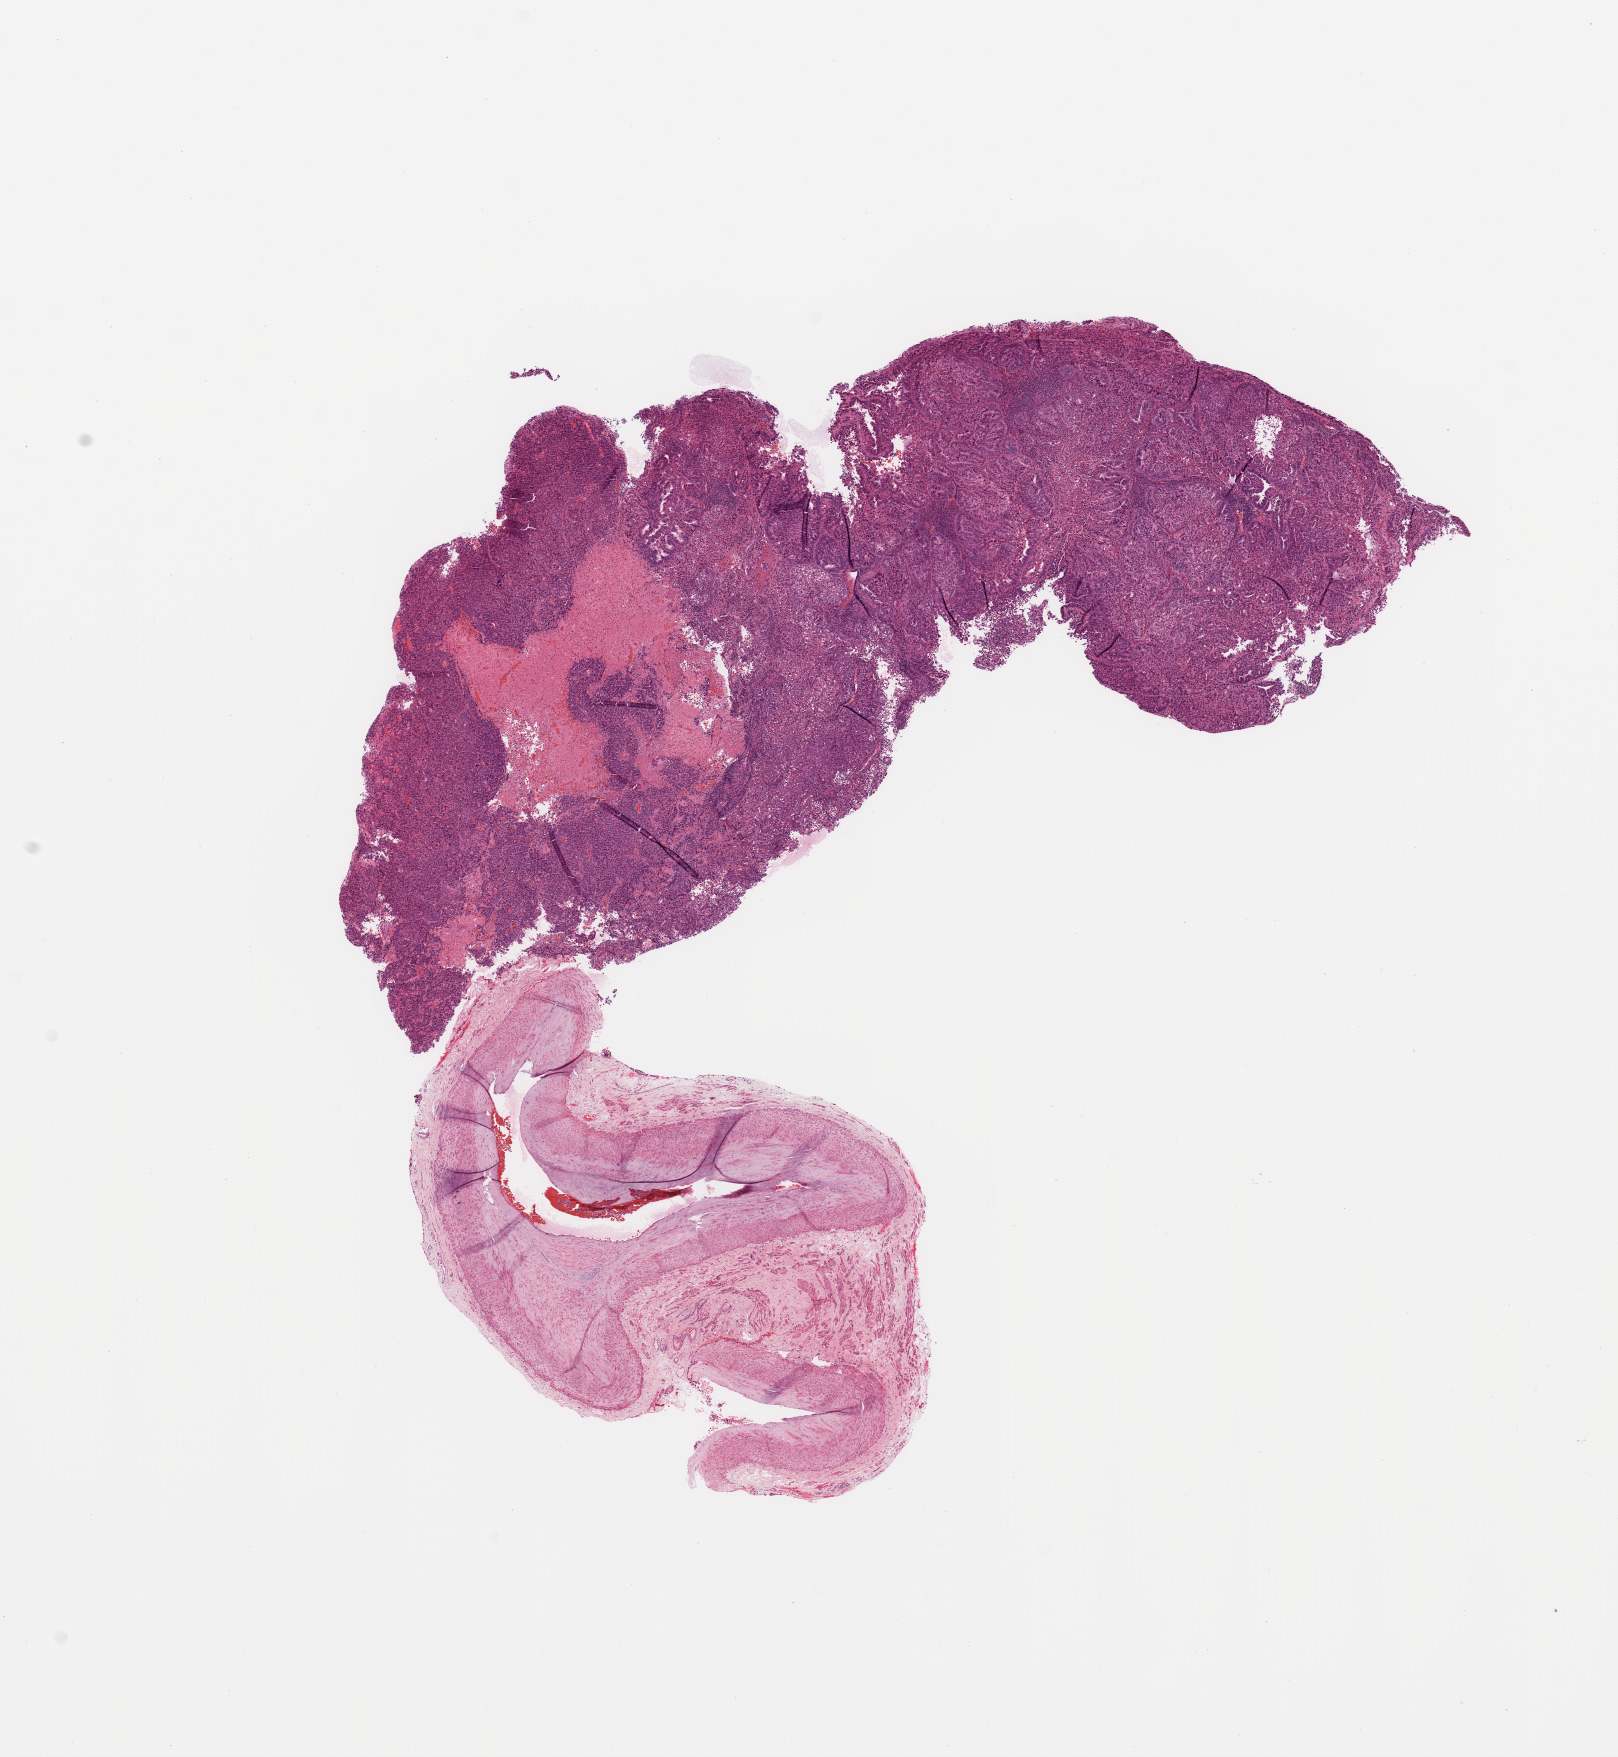
Whole-slide histology image, Hematoxylin and eosin (H&E) stained — low-resolution overview of the scanned area, about 12.8 x 13.9 mm; tumour tissue sample, uterus. 60-year-old female patient. Histologic grade: G3 (poorly differentiated).
AJCC pathologic stage: I. Histologic diagnosis: Endometrioid adenocarcinoma, NOS.